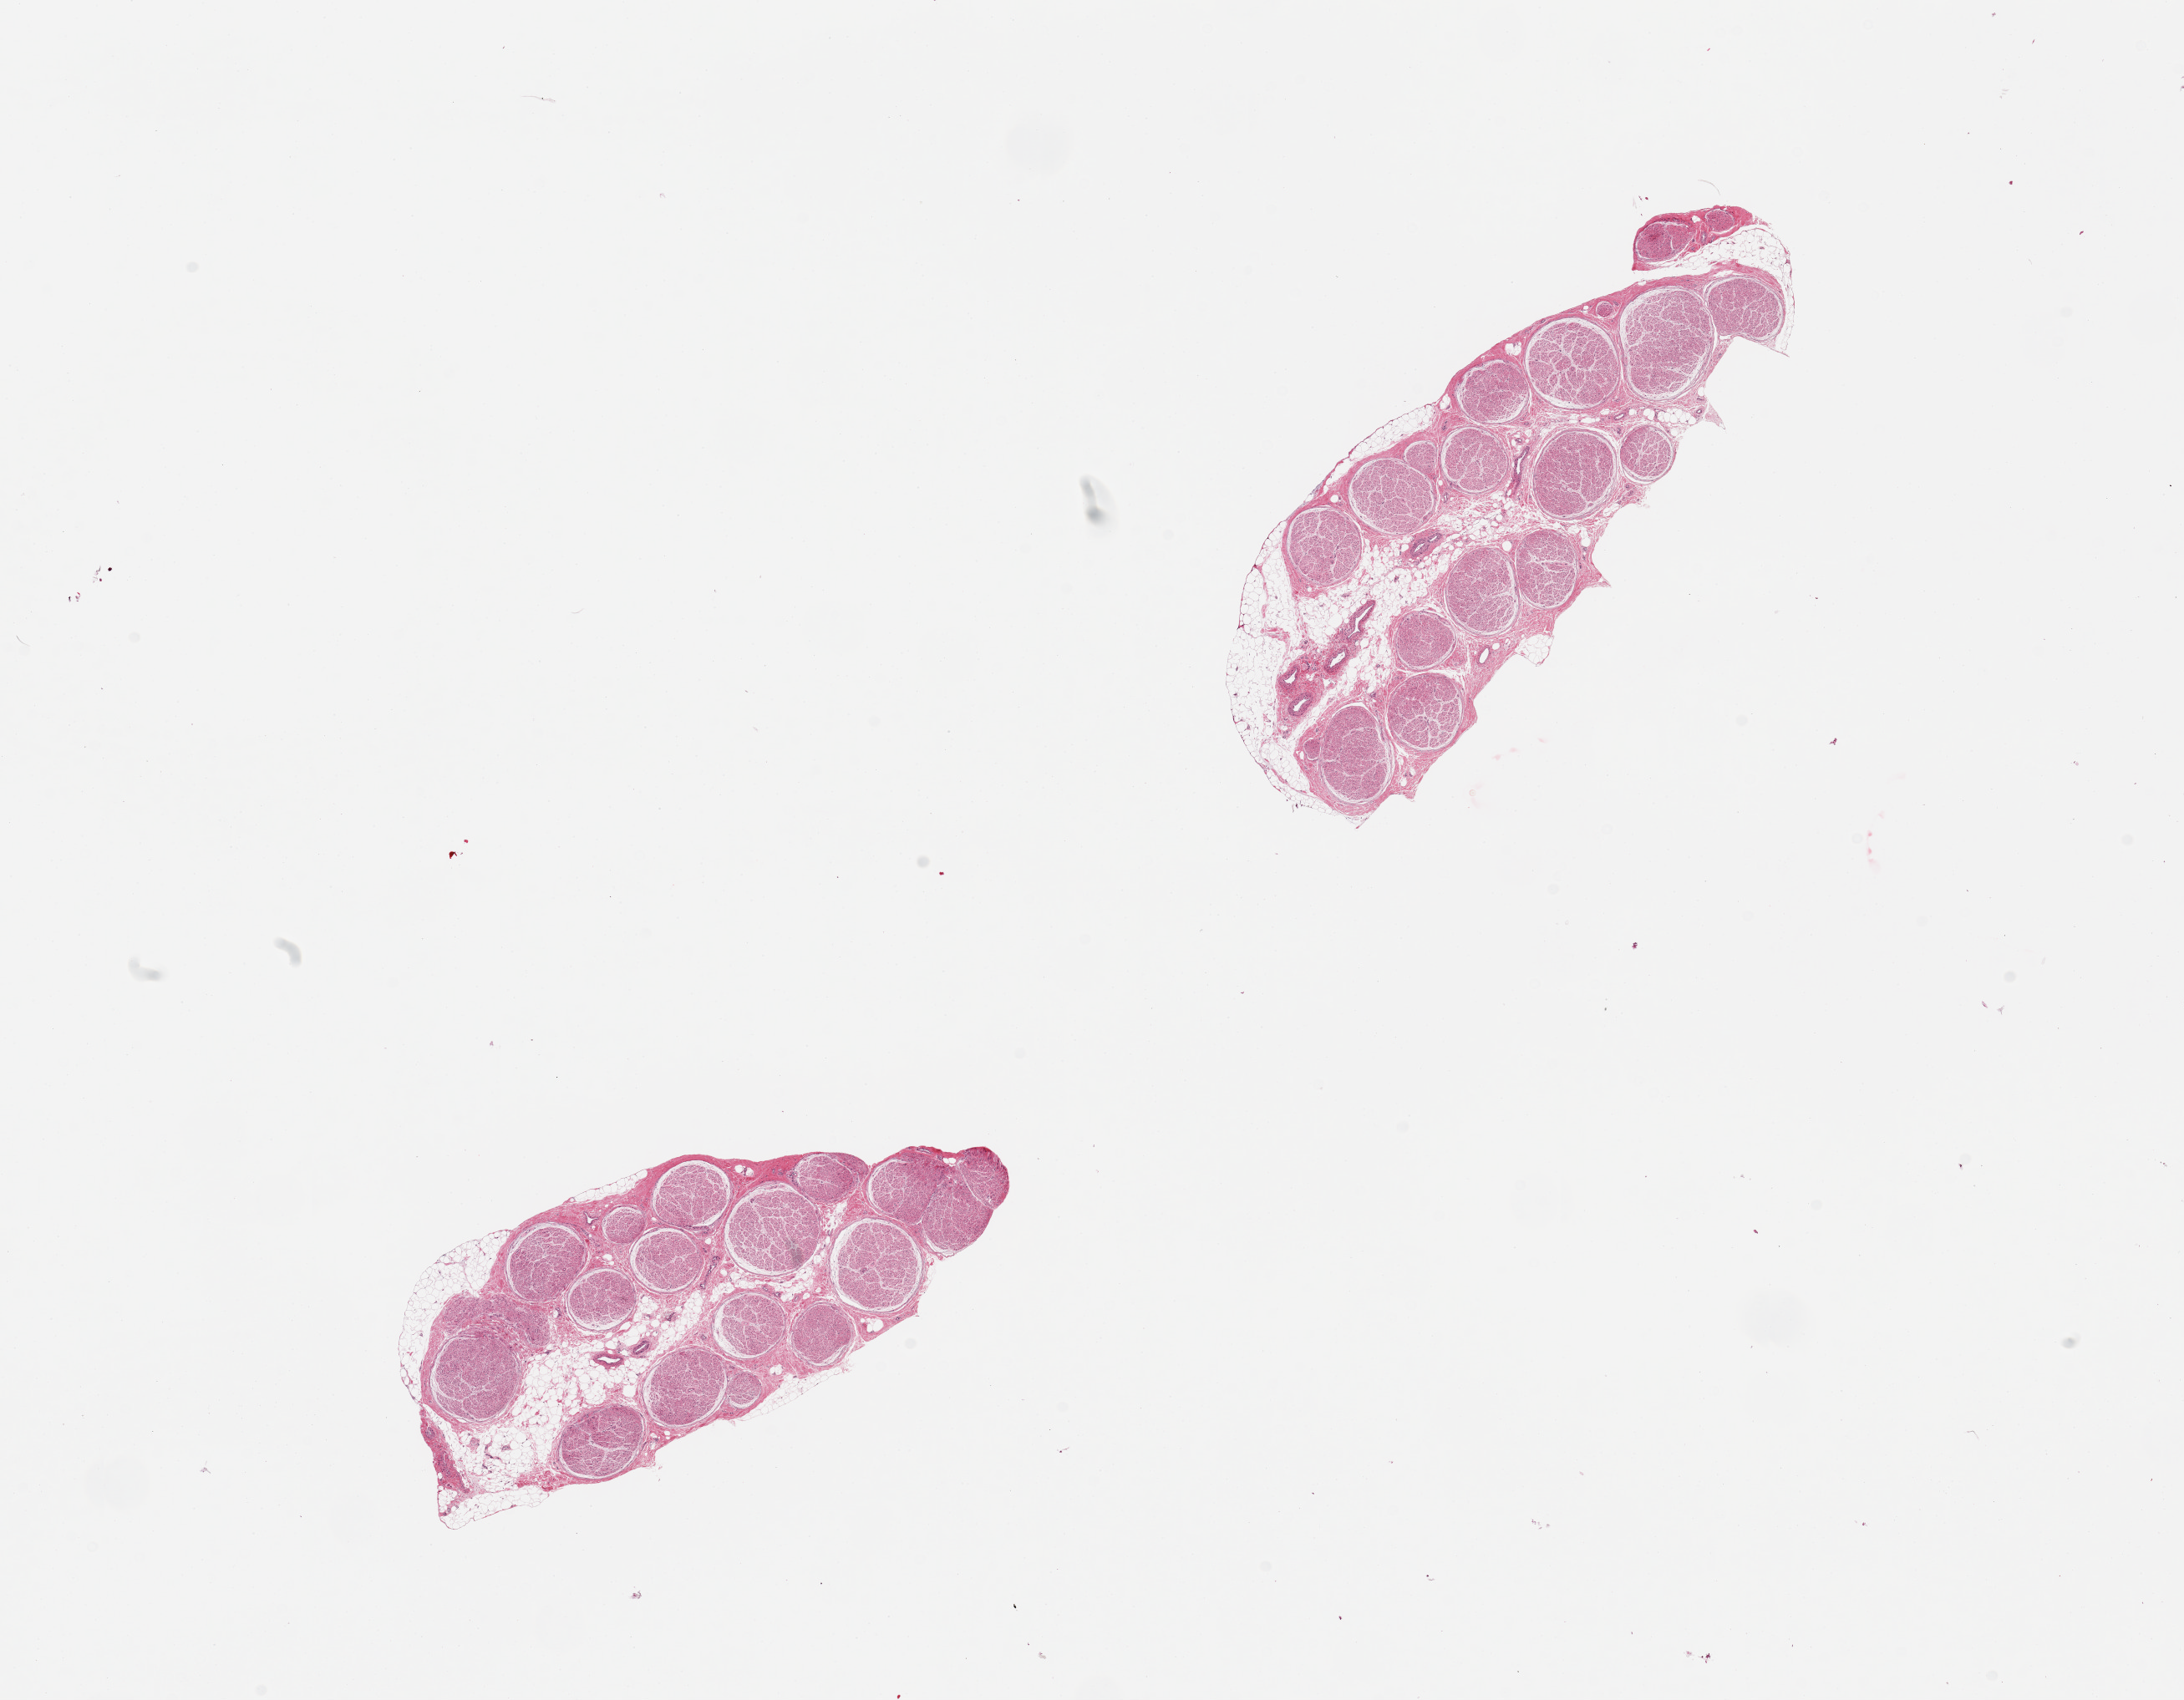
Hematoxylin and eosin (H&E) whole-slide image, brightfield — low-resolution overview of the scanned area, about 20.7 x 16.1 mm (from a 20x scan); PAXgene-fixed paraffin-embedded (PFPE) section; section of tibial nerve (target tissue); tissue donor sample. Donor: female.
Pathologist's review note for this sample: 2 pieces, trace ahderent fat, good specimens.